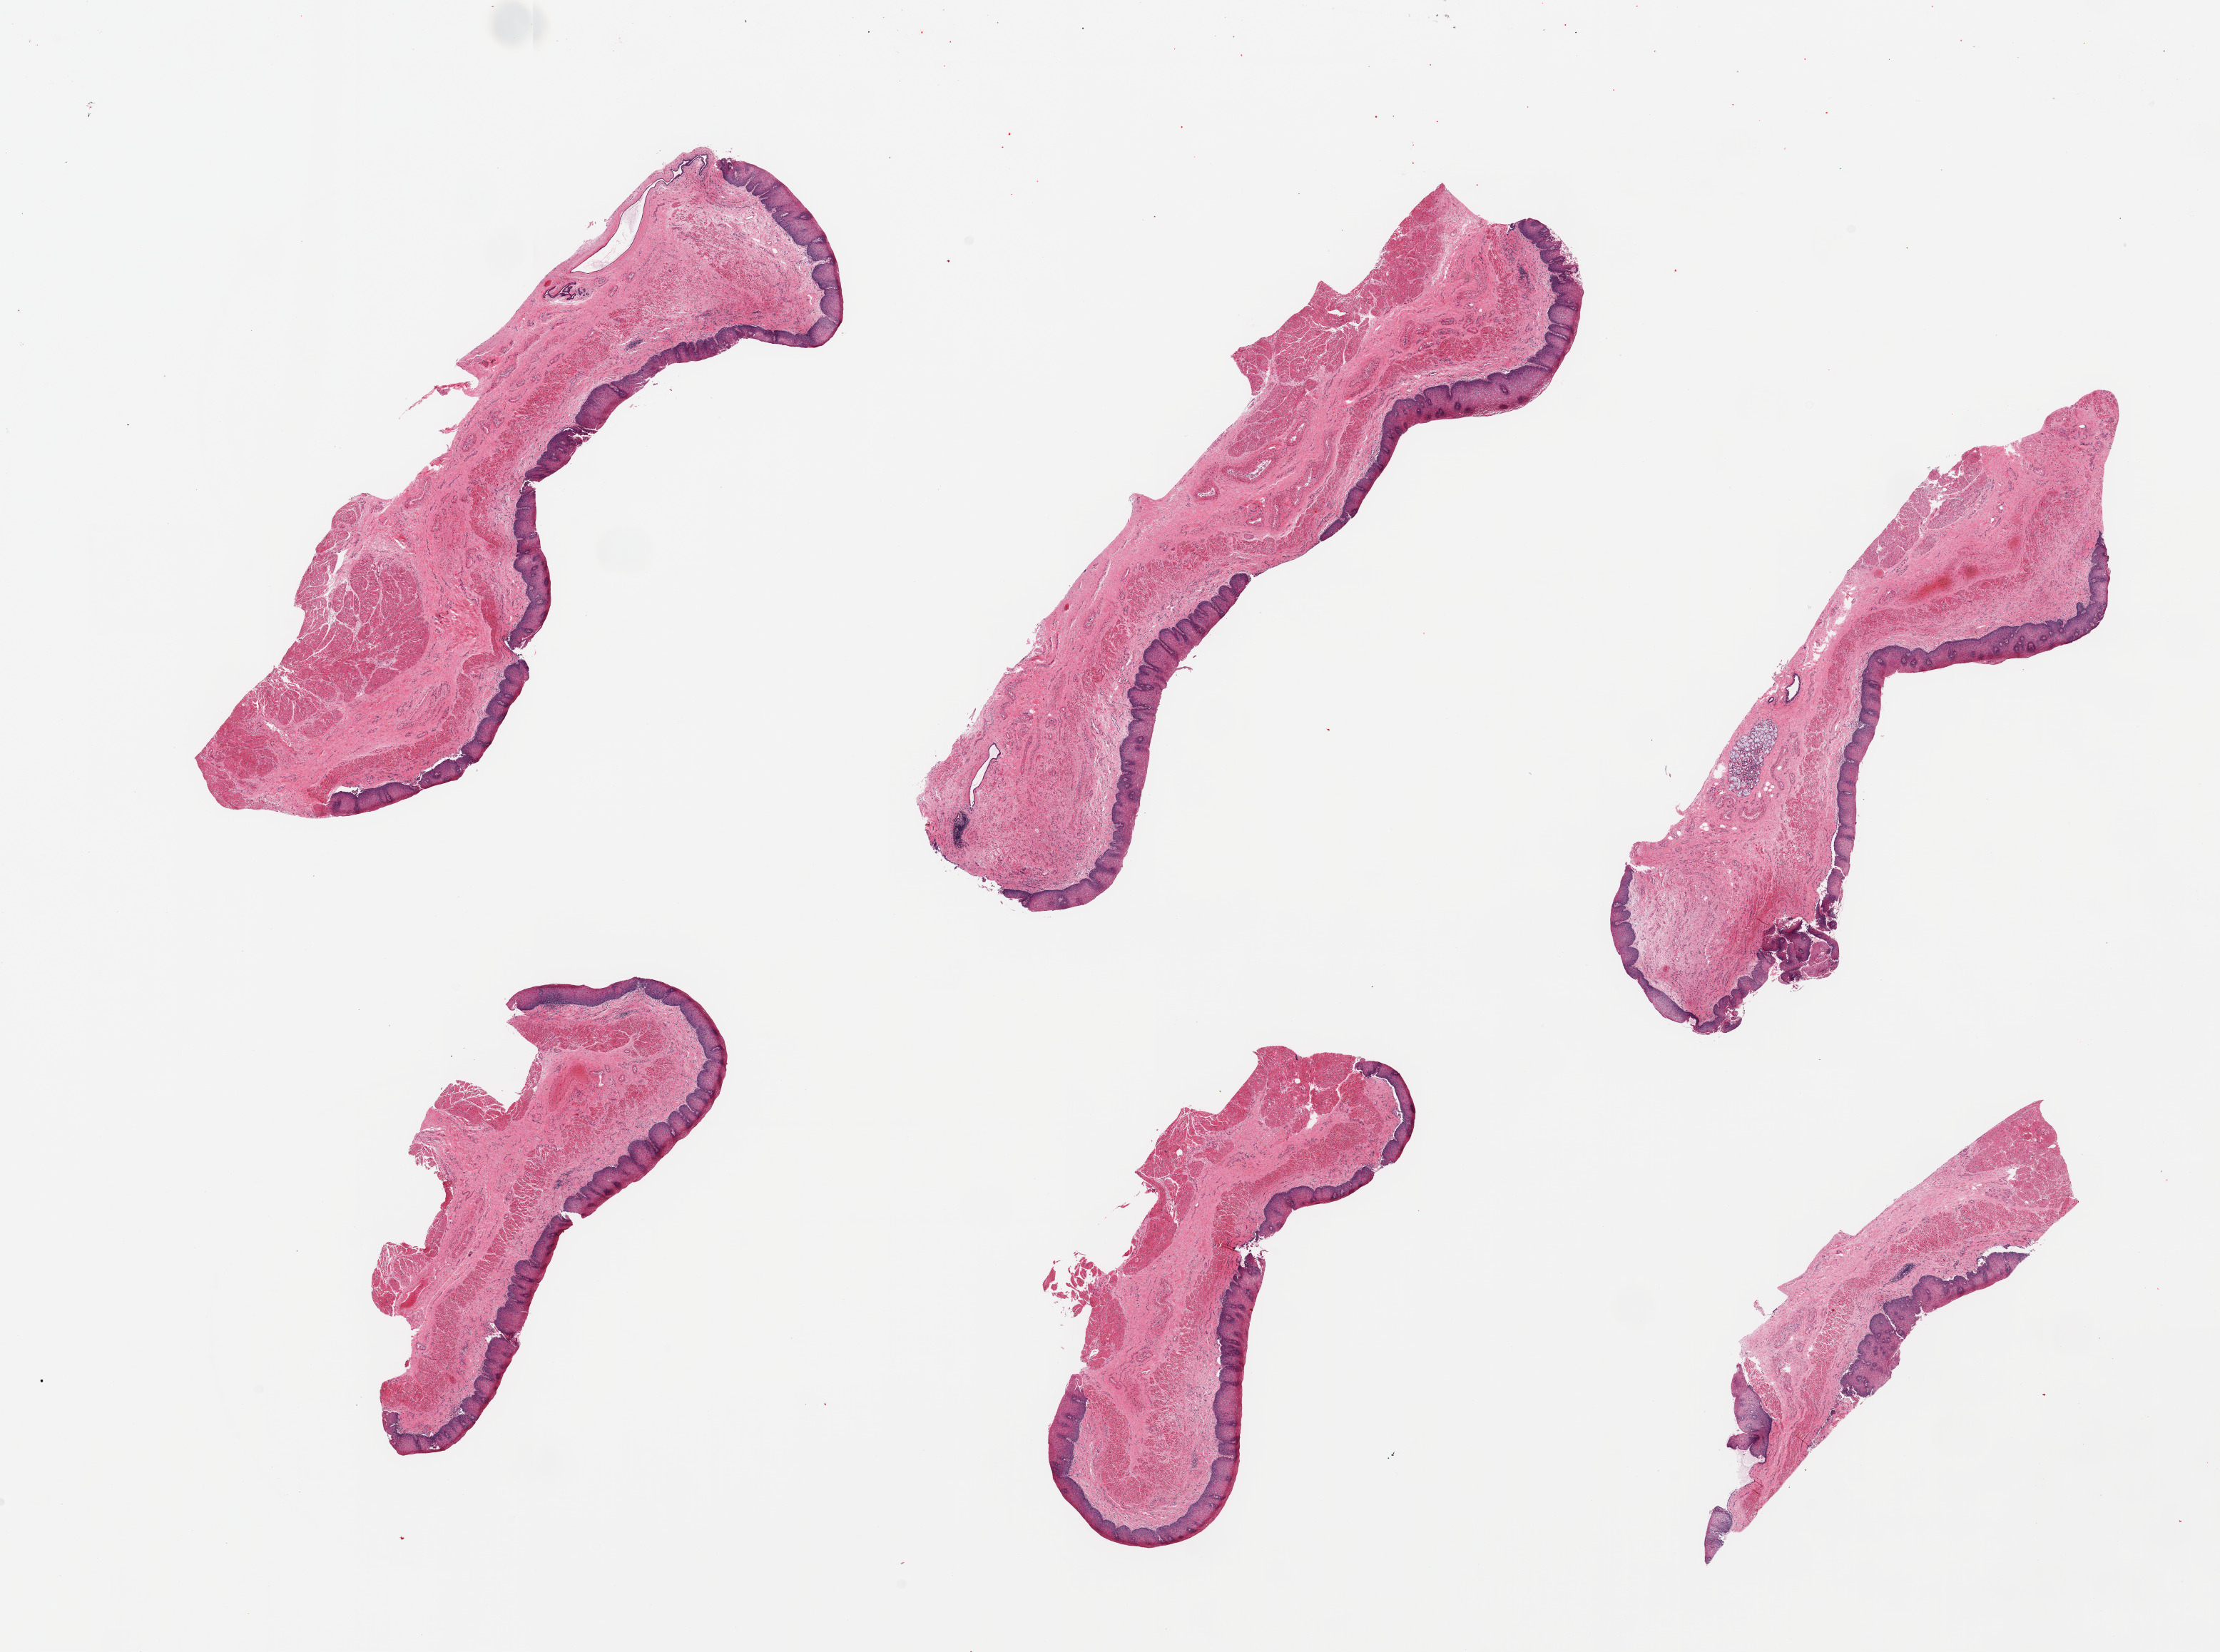
Whole-slide image, haematoxylin and eosin stain, low-resolution overview of the scanned area, about 24.6 x 18.3 mm (acquisition: 20x scan), PAXgene-fixed, paraffin-embedded tissue, sampled site (target tissue): esophageal mucous membrane, donor tissue sample. Donor: male.
Review note (as recorded): 6 pieces; includes portion of muscularis, few dilated glands.